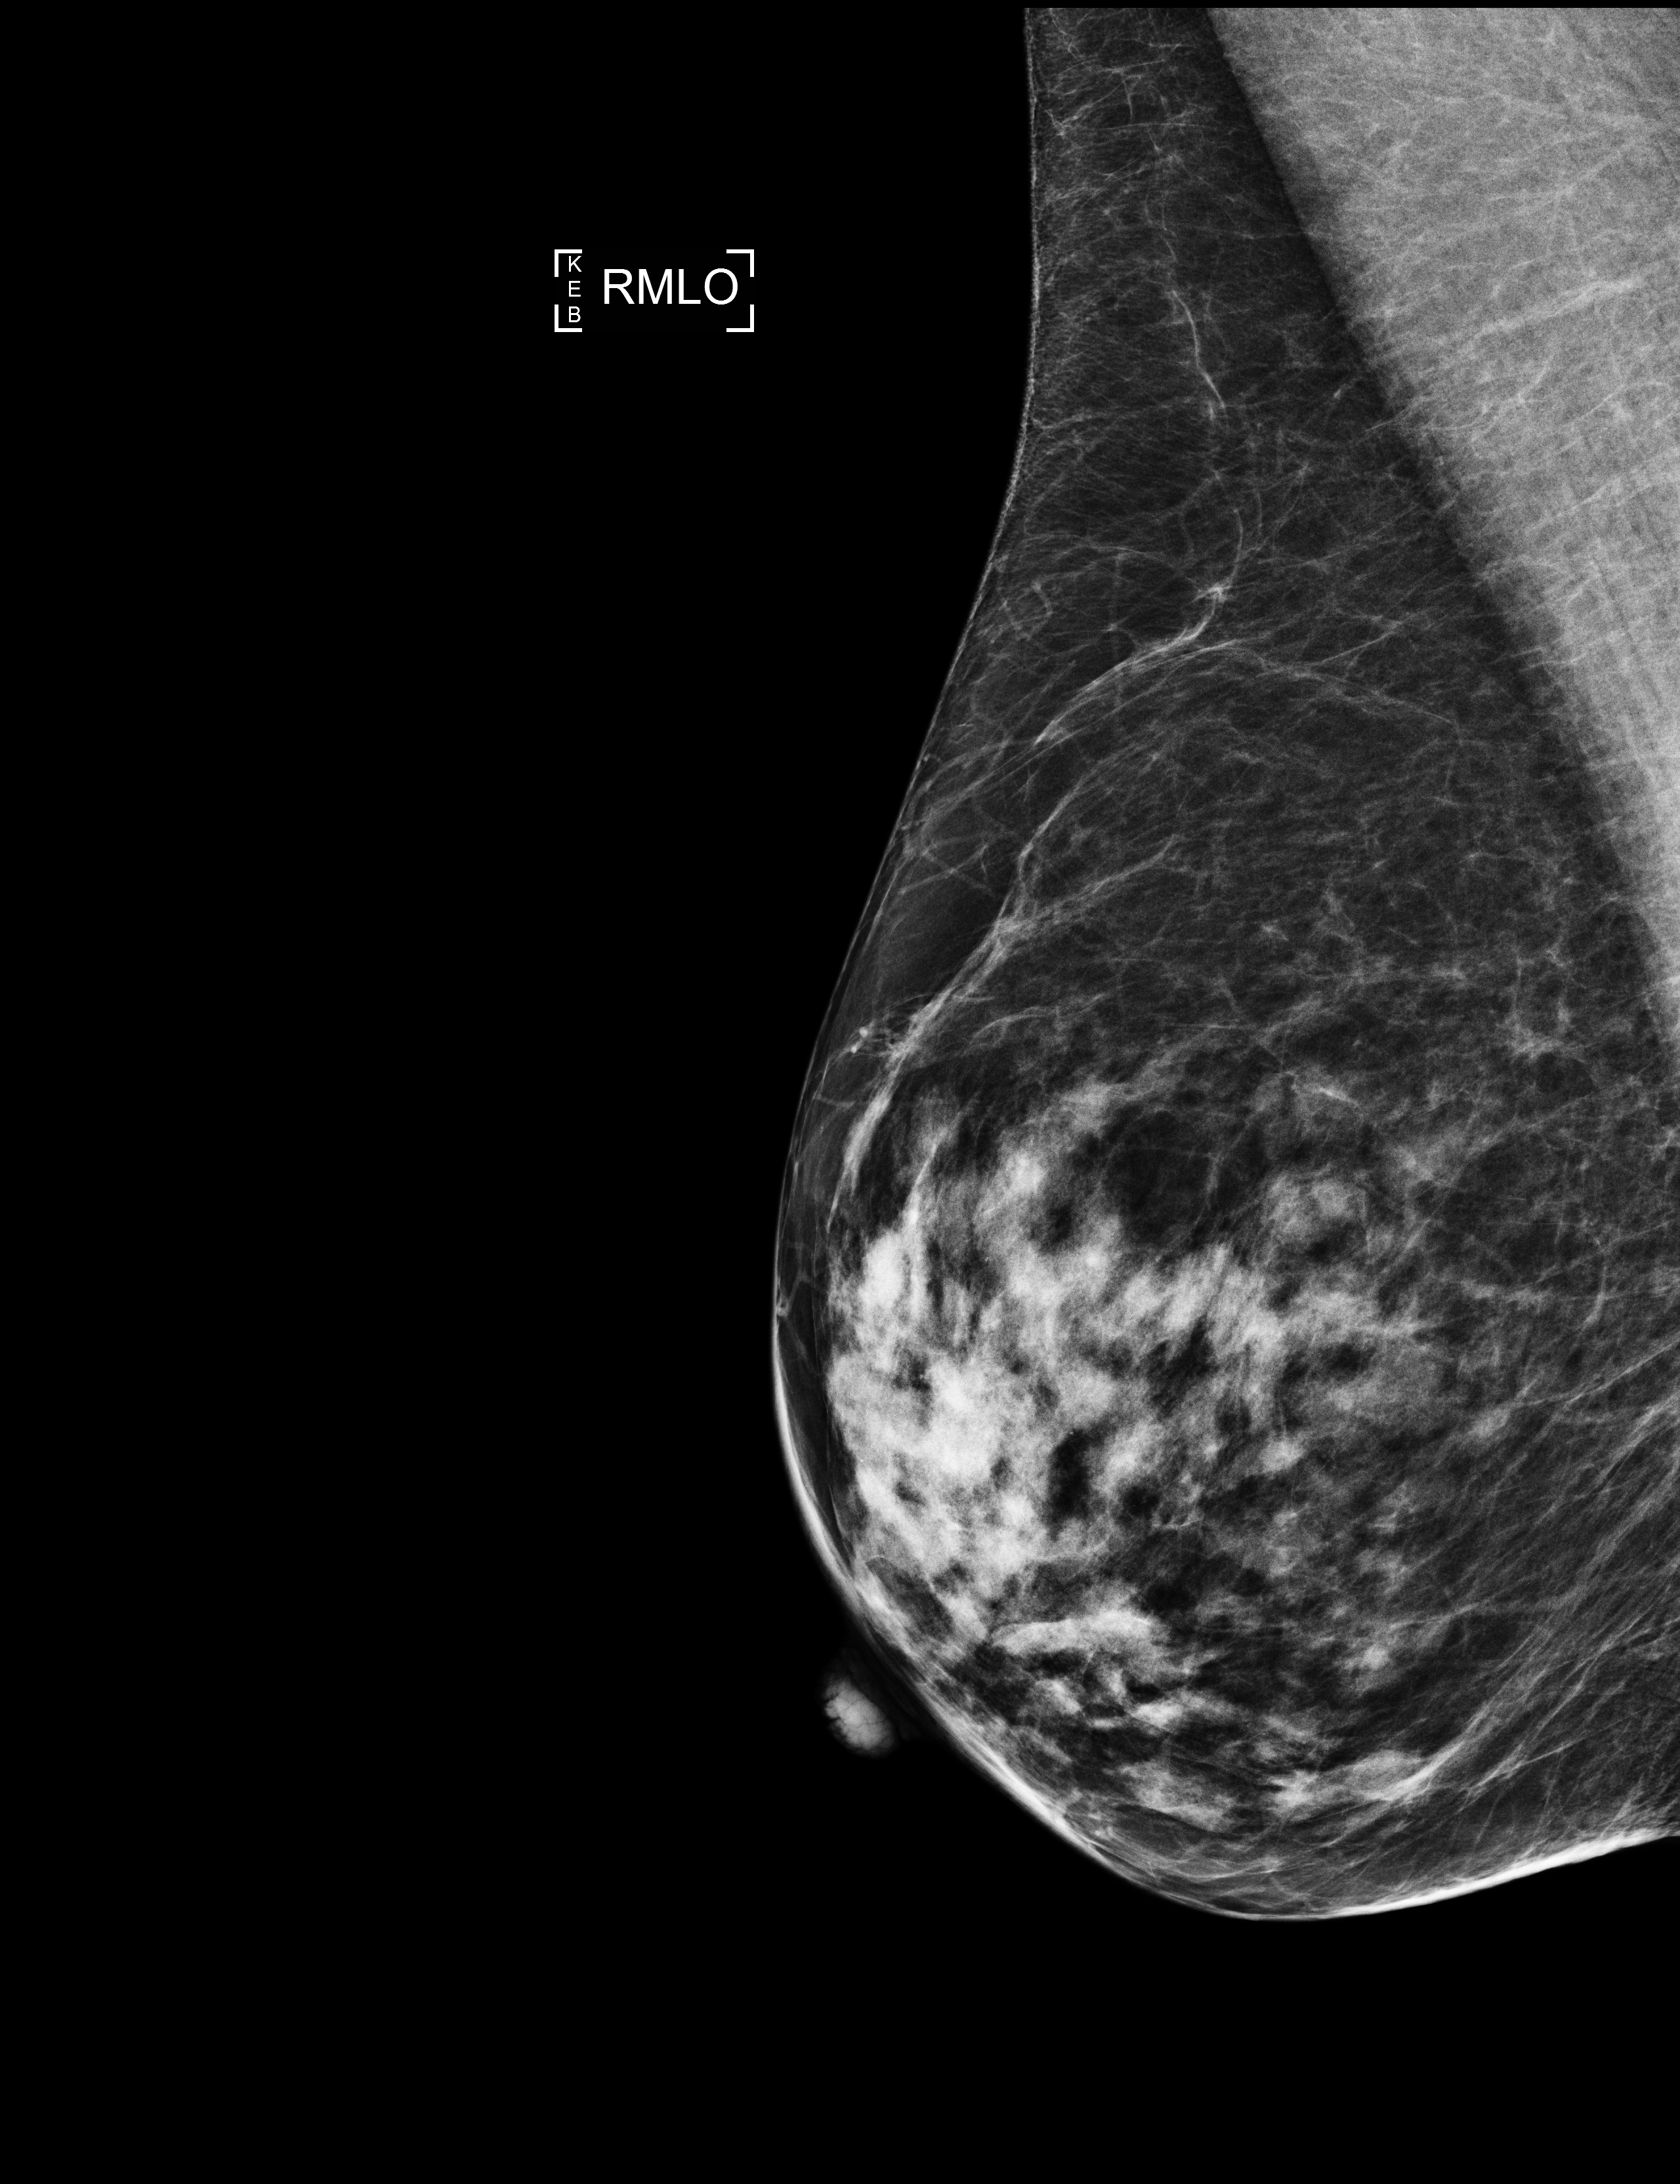
Full-field digital mammogram (FFDM); right breast; MLO view; screening examination. Female patient, age 72 years.
- BI-RADS breast density category at the screening exam (both breasts, scale 1–4): 3
- final BI-RADS assessment for this screening round (tomosynthesis exam, both breasts): category 1
- recall: no recall after this screen